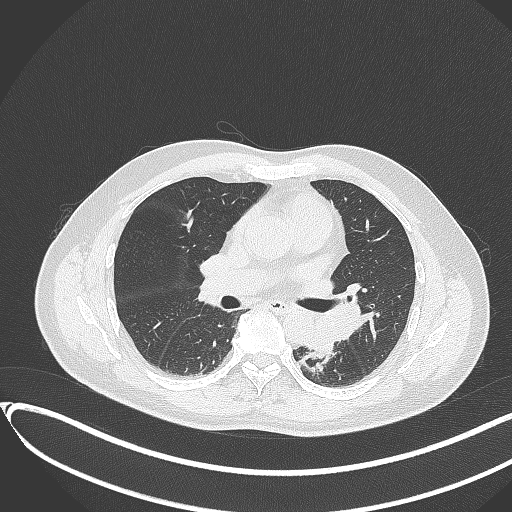
Chest CT, one axial slice. Position 190 of 417 along the scan axis. Lung window (W 1500 / L -600 HU). 512 × 512 image matrix, field of view 400 × 400 mm. Male patient, age 54 years. Case-level facts recorded for this patient, not image findings: clinical TNM (as recorded): T3 N0 M0.
Structures marked on this image (rectangle marked by the reading radiologist):
- lung tumour (recorded histology: squamous cell carcinoma): bounding box (x1, y1, x2, y2) in pixels: (309, 319, 338, 365)